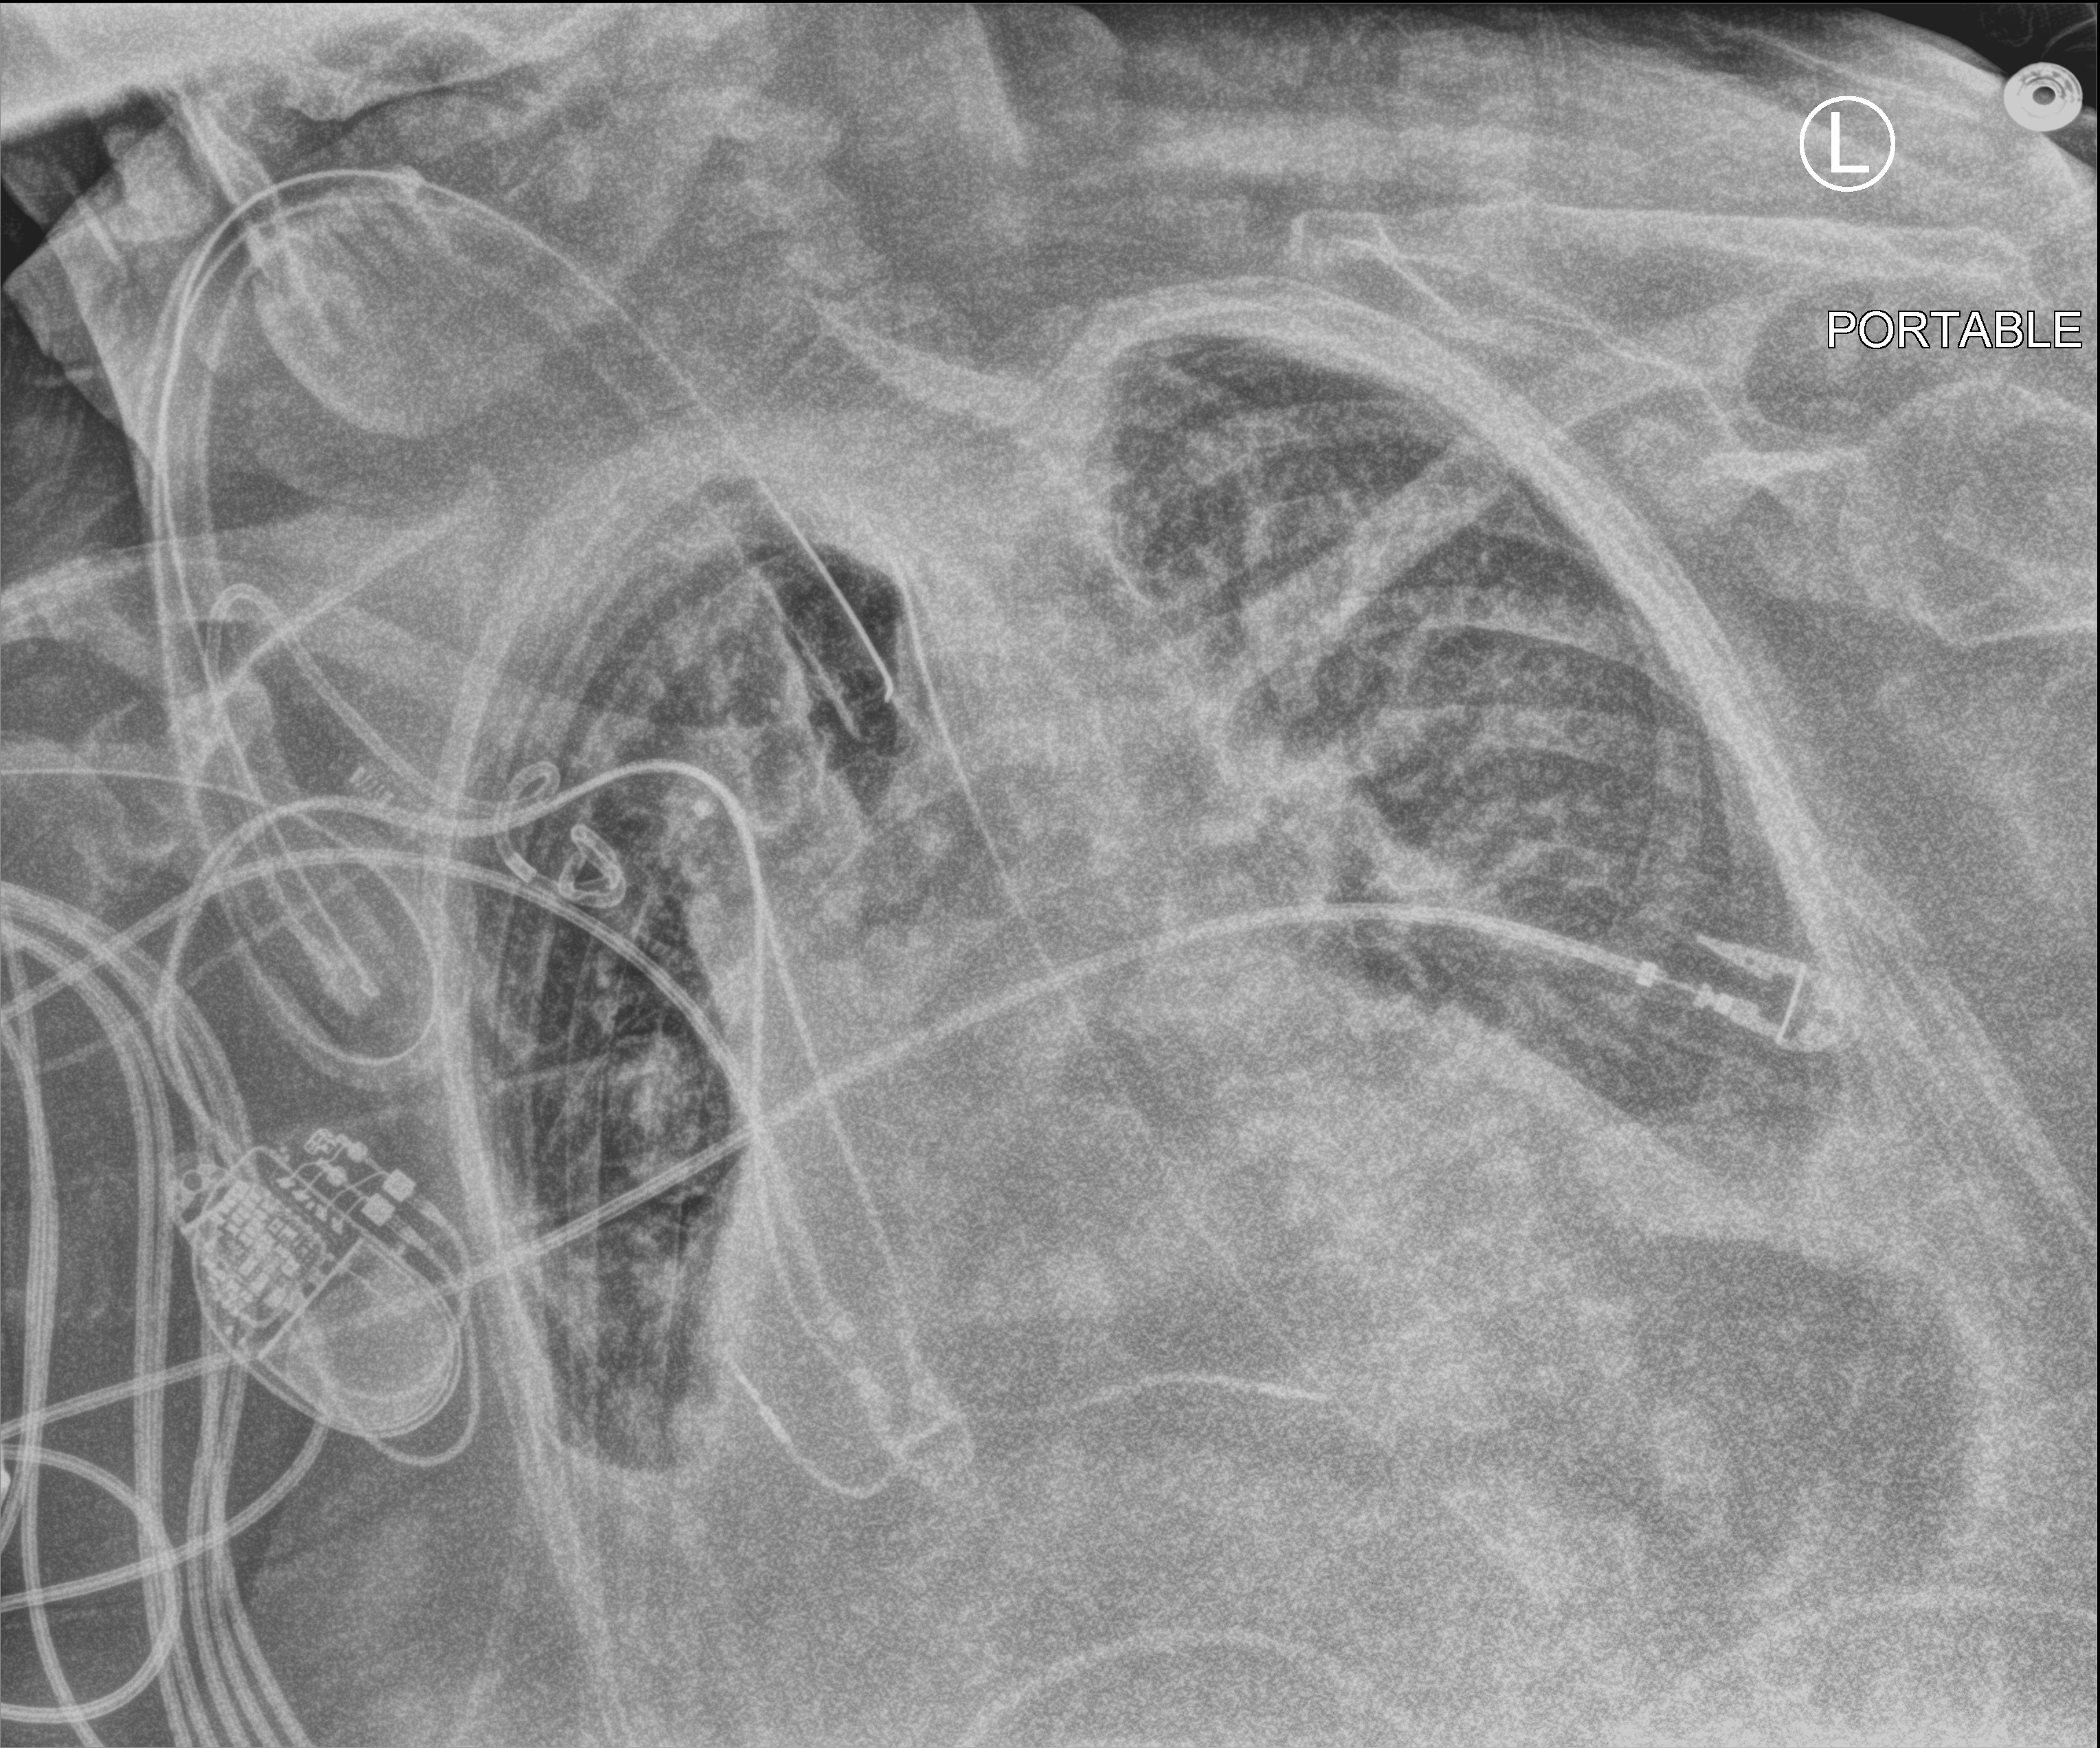
Bedside chest radiograph (computed radiography), anteroposterior (AP) projection. Female patient hospitalised with COVID-19, age 75–90 years.
From the hospital-stay record, not from the radiograph (when in the stay this image was taken is not recorded): length of hospital stay: 21 days; mechanically ventilated during this hospital stay: yes.